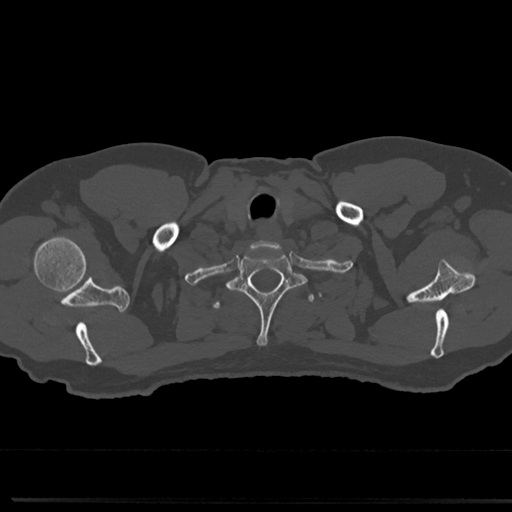
CT including the spine, one axial slice; slice 673 of 817 in the series (ordered by position); reconstruction kernel Br40s/3; 120 kVp; bone window (W 1800 / L 400 HU); 512 × 512 image matrix, field of view 355 × 355 mm. Patient: male, 61 years. From the clinical record (not read from this slice): primary cancer: prostate.
Annotated regions visible in this slice (semi-automatic segmentation, software-assisted and operator-edited):
- T1 vertebra: bounding box (x1, y1, x2, y2) in pixels: (232, 249, 301, 346)
- T2 vertebra: (212, 291, 315, 314)